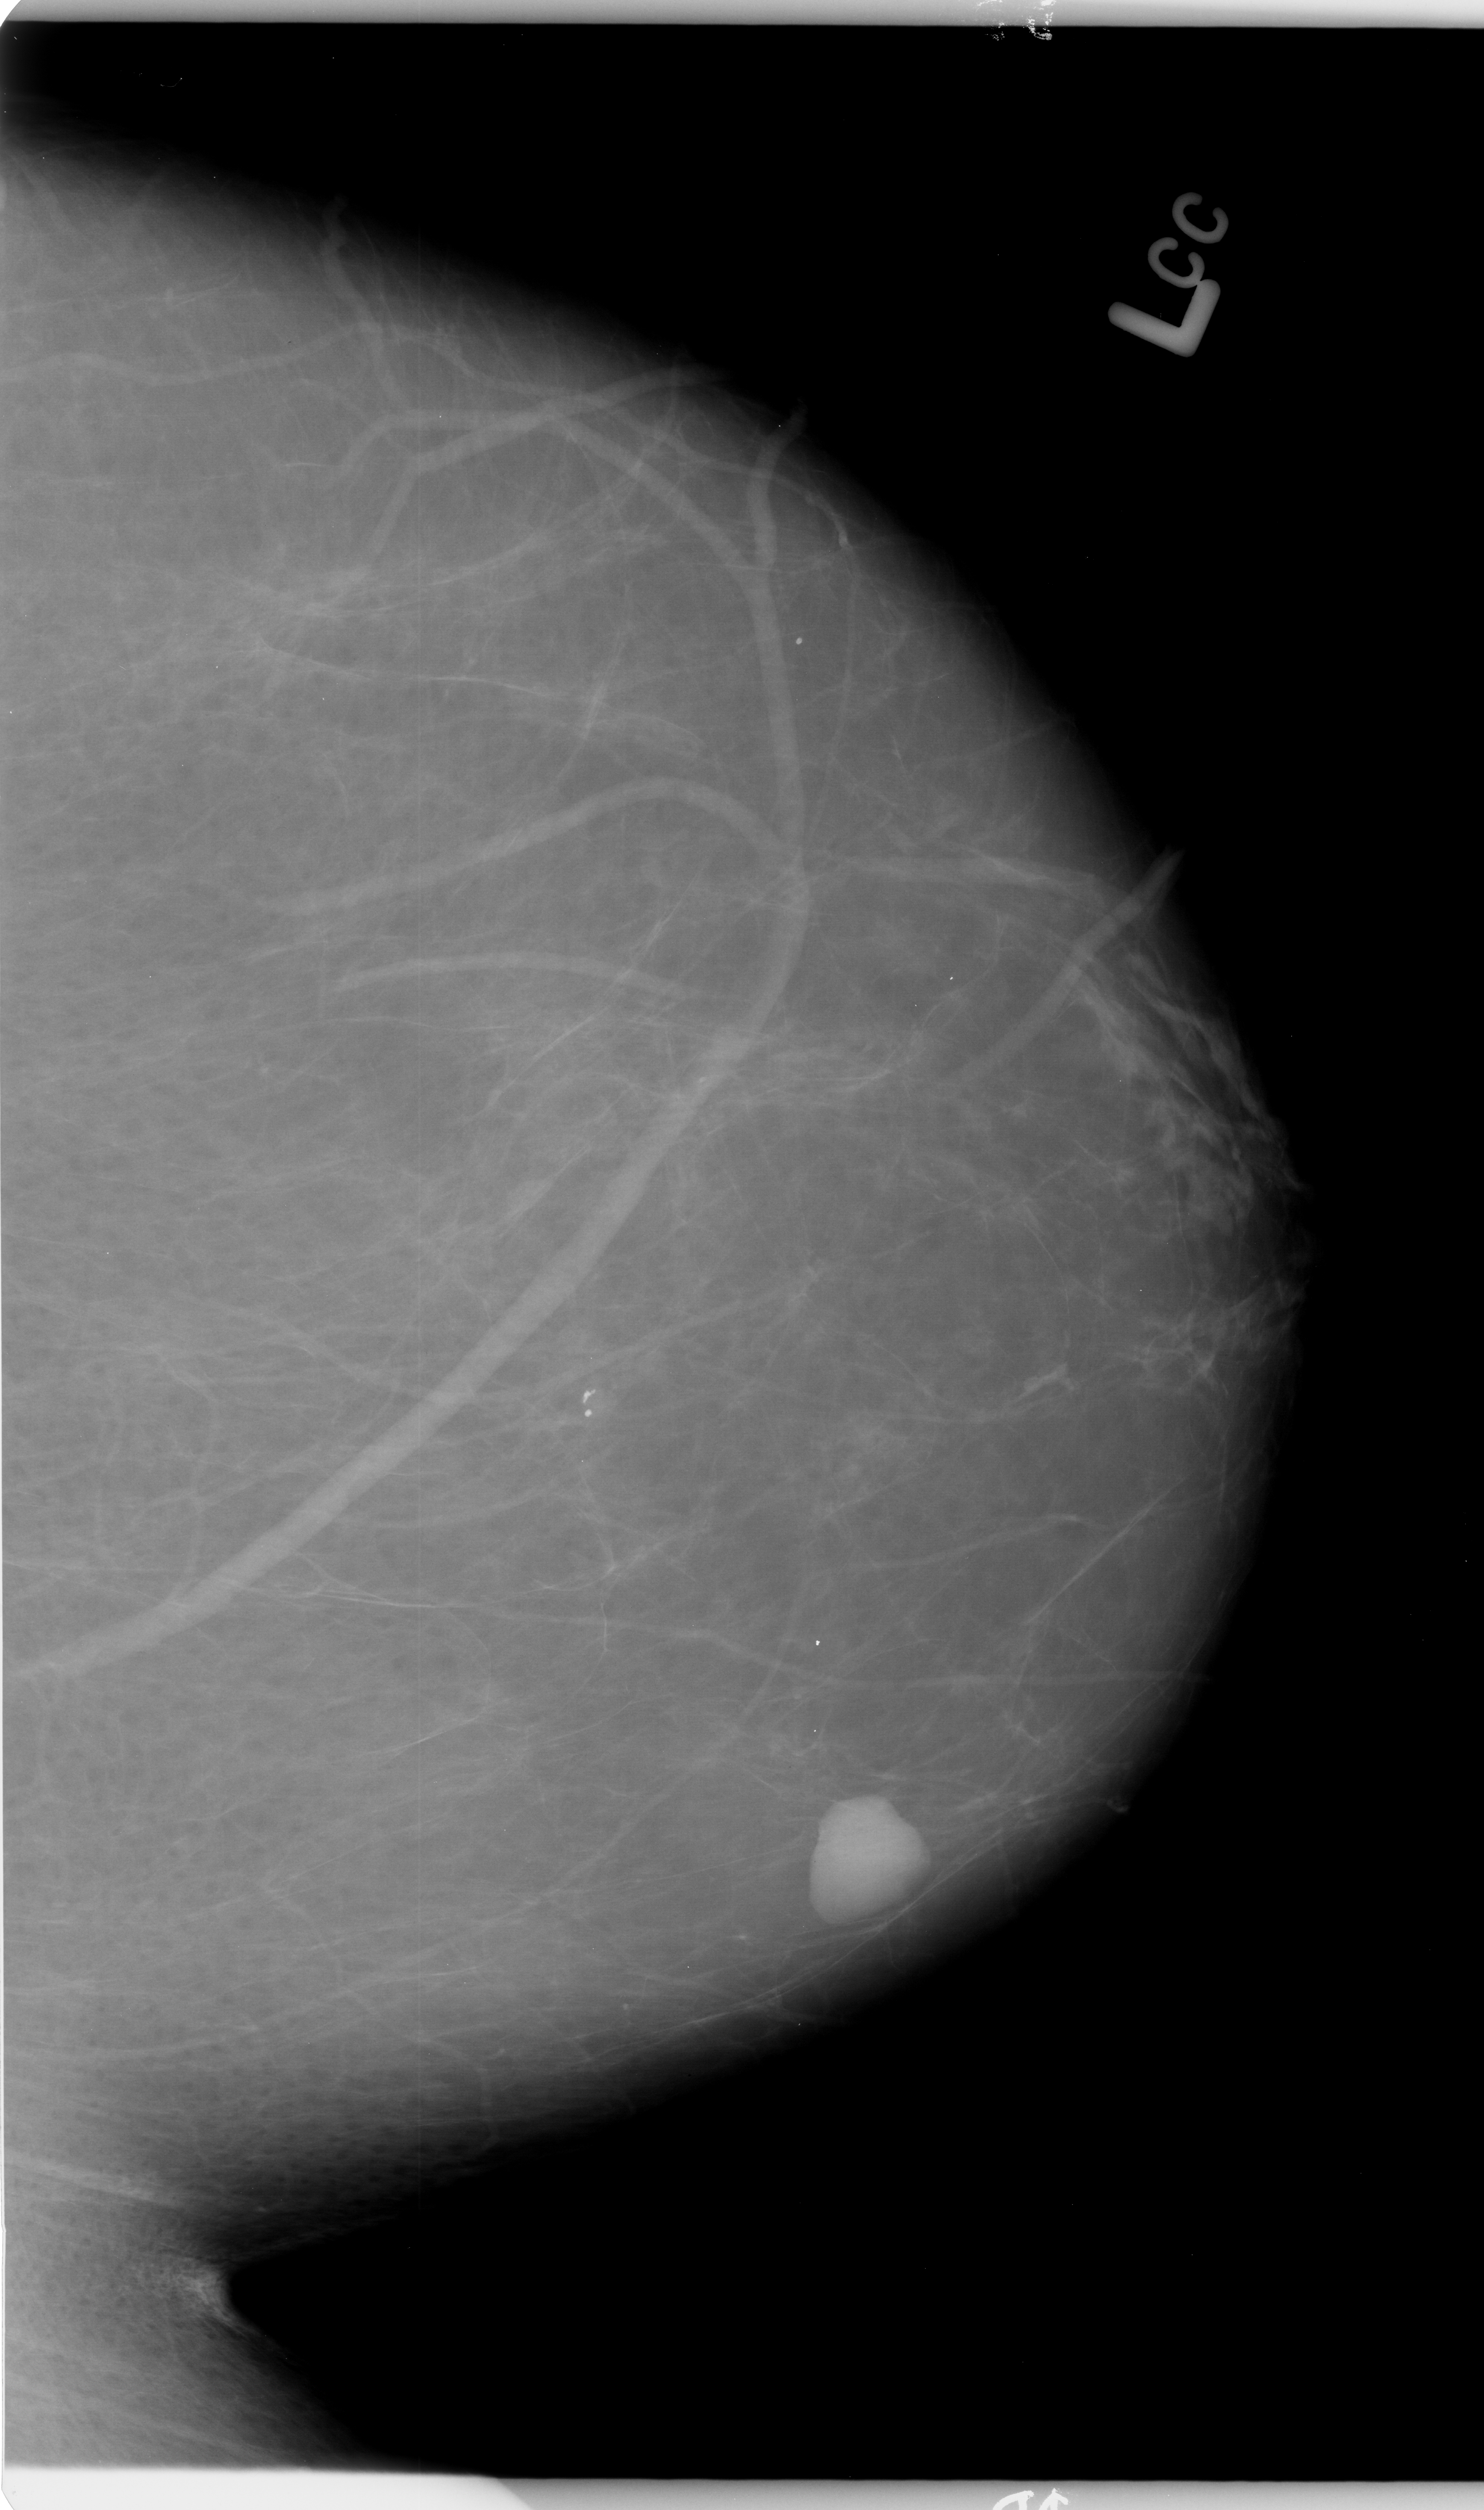
Mammogram (digitized film), left breast, CC view, breast composition: almost entirely fatty (BI-RADS density category 1 of 4).
Abnormality record for this image: mass, shape oval, margins circumscribed; BI-RADS assessment category 4; subtlety rating 5 on a 1 (subtle) to 5 (obvious) scale; pathology (as recorded): benign.